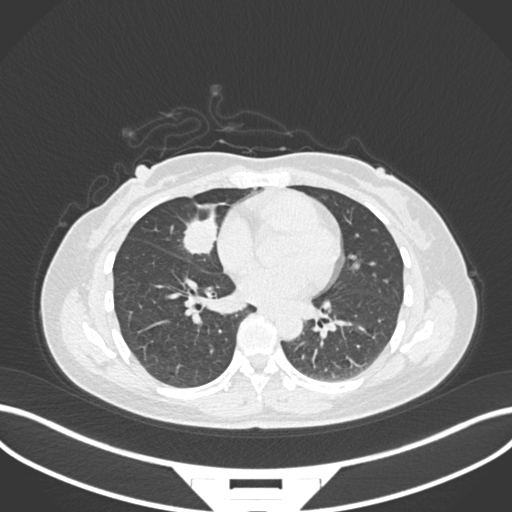
Chest CT, one axial slice; reconstruction kernel B30f; lung window (W 1500 / L -600 HU); 1 mm slice thickness; 512 × 512 image matrix. Patient: female, 43 years. From the clinical record (not read from this slice): clinical TNM (as recorded): T1c N3 M1; histopathological grade: G1.
Structures marked on this image (bounding box drawn by a radiologist):
- lung tumour (recorded histology: adenocarcinoma): bounding box [x1, y1, x2, y2] px = [178, 211, 222, 261]